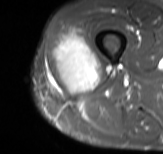
MRI of an extremity soft-tissue mass, one axial slice. Slice 29 of 61 in the series (ordered by position). STIR. MR volume resampled by the dataset authors to the PET/CT grid (not the native acquisition matrix). 3.27 mm slice thickness. 163 × 154 image matrix, field of view 159 × 150 mm. Male patient. From the clinical record (not read from this slice): histological type: poorly differentiated synovial sarcoma; grade: high; site of the primary tumour: right buttock.
Outlined on this slice (expert contour drawn on MRI and transferred to this co-registered scan by the dataset authors):
- gross tumour volume including surrounding oedema: box from (x=52, y=25) to (x=99, y=93) px
- gross tumour volume (mass): (x=53, y=34)–(x=99, y=92)